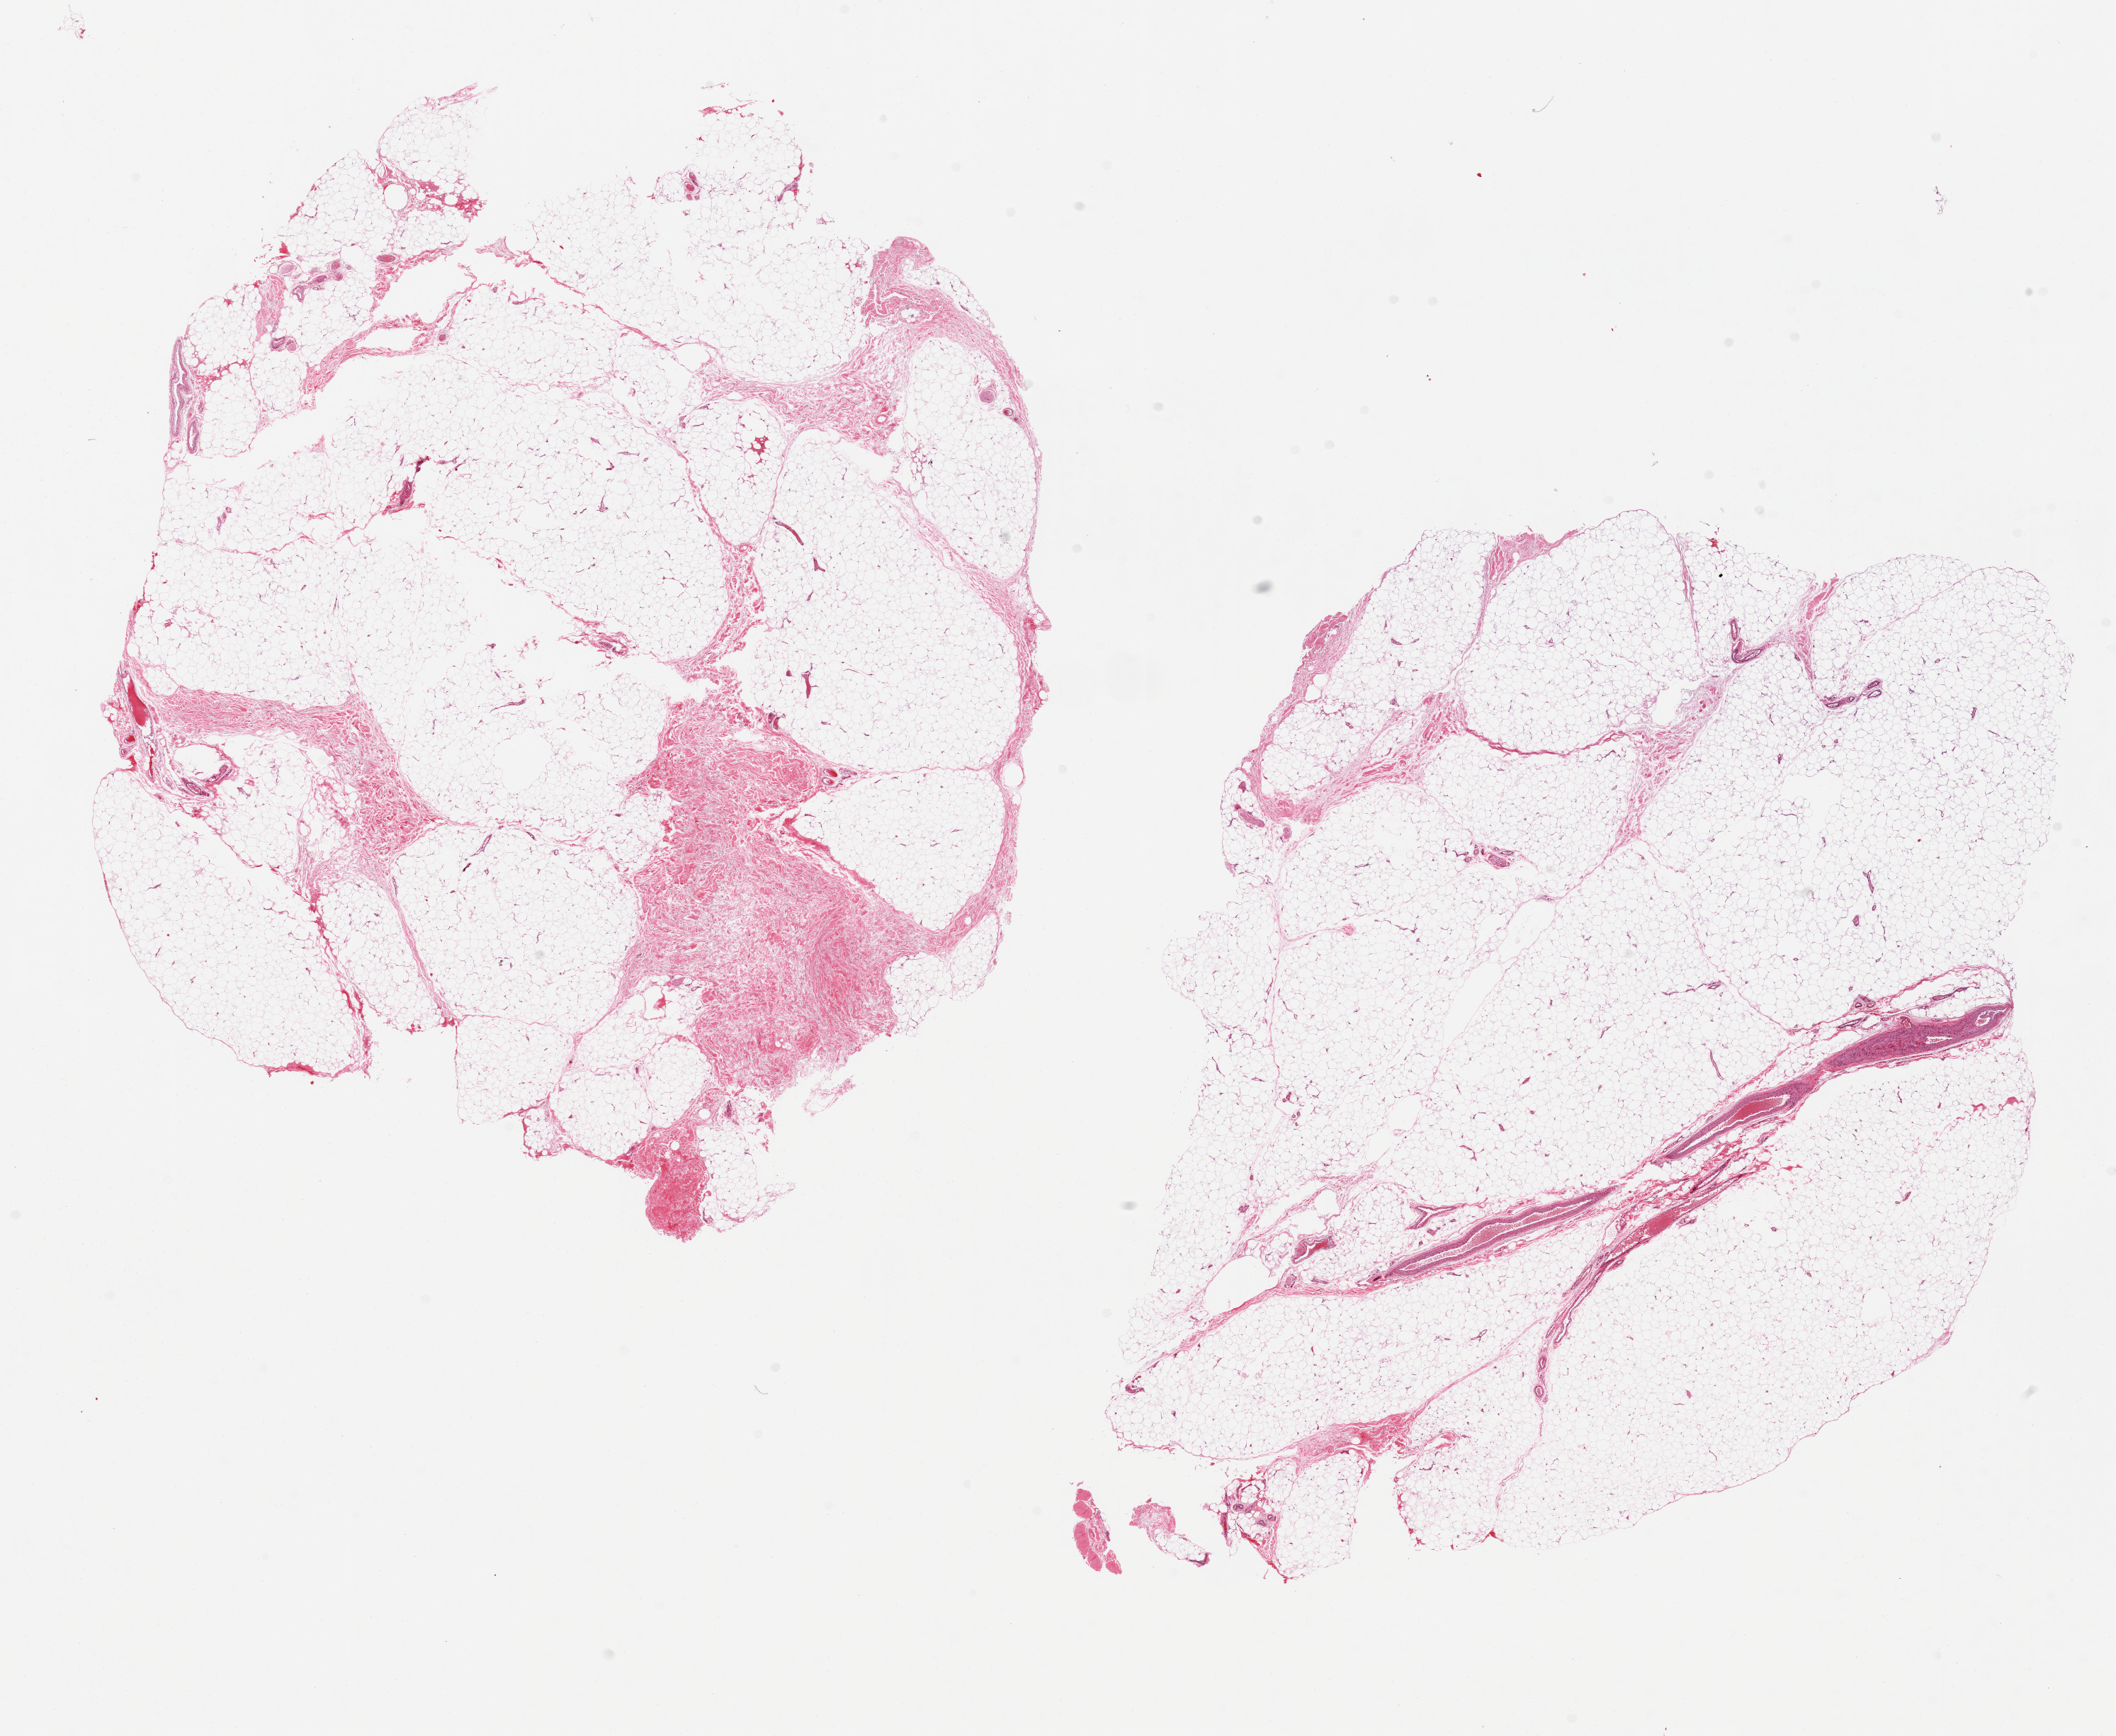
Whole-slide image, H&E stain, brightfield — shown as a low-resolution overview of the whole scanned area (about 23.6 x 19.4 mm), PAXgene-fixed, paraffin-embedded tissue, section of adipose tissue (target tissue), donor tissue sample. Donor: male.
Reviewer comment on this tissue sample: 2 pieces; 20% fibrous tissue in 1 piece.